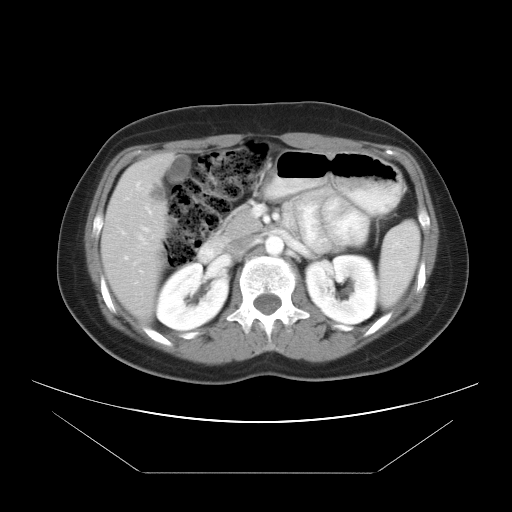
Contrast-enhanced abdominal CT, one axial slice; position 20 of 34 along the scan axis; reconstruction kernel STANDARD; intravenous contrast given; soft-tissue window (W 400 / L 40 HU); 7.5 mm slice thickness; 512 × 512 image matrix. Female patient, age 38 years. From the clinical record (not read from this slice): diagnosis: colorectal cancer liver metastases, imaged before liver resection; multiple liver metastases: yes; largest metastasis: 3.1 cm; disease in both lobes: no.
Outlined on this slice (expert manual segmentation):
- liver: bounding box [x1, y1, x2, y2] px = [101, 154, 172, 323]
- portal vein (with intrahepatic branches): [119, 206, 217, 285]
- liver metastasis: [146, 179, 167, 204]